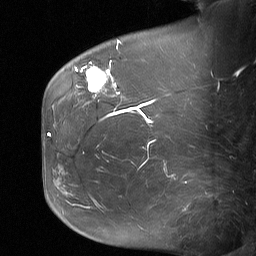
Breast MRI (dynamic contrast-enhanced), one sagittal slice. Position 19 of 64 along the scan axis. Dynamic contrast-enhanced study with each time point stored as its own series, time point 2 of 3 at this slice position (early post-contrast, ordered by acquisition time). 1.5 T. TE 4.8 ms, TR 27 ms. 256 × 256 image matrix, field of view 200 × 200 mm. Patient: female, 60 years. From the clinical record (not read from this slice): setting: breast cancer imaged before/during neoadjuvant chemotherapy; receptor status: HR-positive, HER2-negative.
Annotated regions visible in this slice (semi-automatically segmented with operator editing):
- analysis volume of interest (the breast-tissue region the enhancement analysis was run in; not a lesion): bounding box (x1, y1, x2, y2) in pixels: (79, 50, 122, 99)
- tumour enhancement mask (voxels above the 90 % enhancement threshold inside the analysis volume of interest): (80, 62, 119, 93)